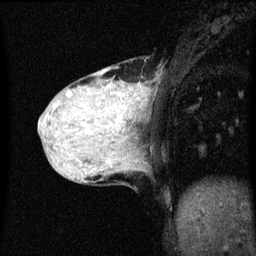
Breast MRI (dynamic contrast-enhanced), one sagittal slice; position 18 of 60 along the scan axis; dynamic contrast-enhanced series, image 2 of 3 at this slice position (ordered by acquisition); 1.5 T; TE 4.2 ms, TR 8.4 ms; 2 mm slice thickness; 256 × 256 image matrix, field of view 200 × 200 mm. Patient: female, 36 years.
Outlined on this slice (semi-automatic segmentation, software-assisted and operator-edited):
- analysis volume of interest (the breast-tissue region the enhancement analysis was run in; not a lesion): box from (x=48, y=68) to (x=151, y=151) px
- tumour enhancement mask (voxels above the 70 % enhancement threshold inside the analysis volume of interest): (x=58, y=86)–(x=141, y=103)